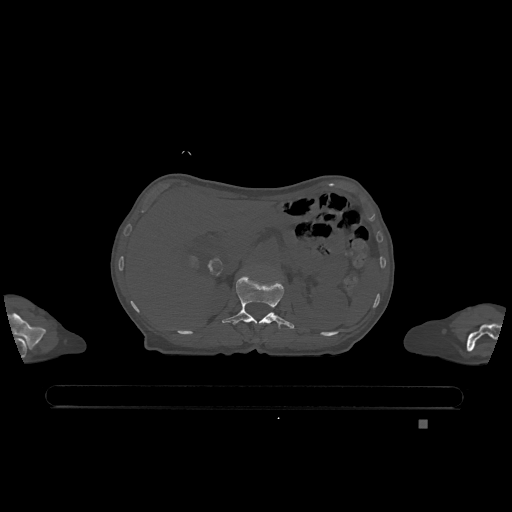
CT including the spine, one axial slice. Position 472 of 1317 along the scan axis. Bone window (W 1800 / L 400 HU). 0.5 mm slice thickness. 512 × 512 image matrix, field of view 500 × 500 mm. Patient: female, 74 years. Case-level facts recorded for this patient, not image findings: primary cancer: lung.
Outlined on this slice (semi-automatic segmentation, software-assisted and operator-edited):
- L1 vertebra: bounding box (x1, y1, x2, y2) in pixels: (222, 275, 294, 329)